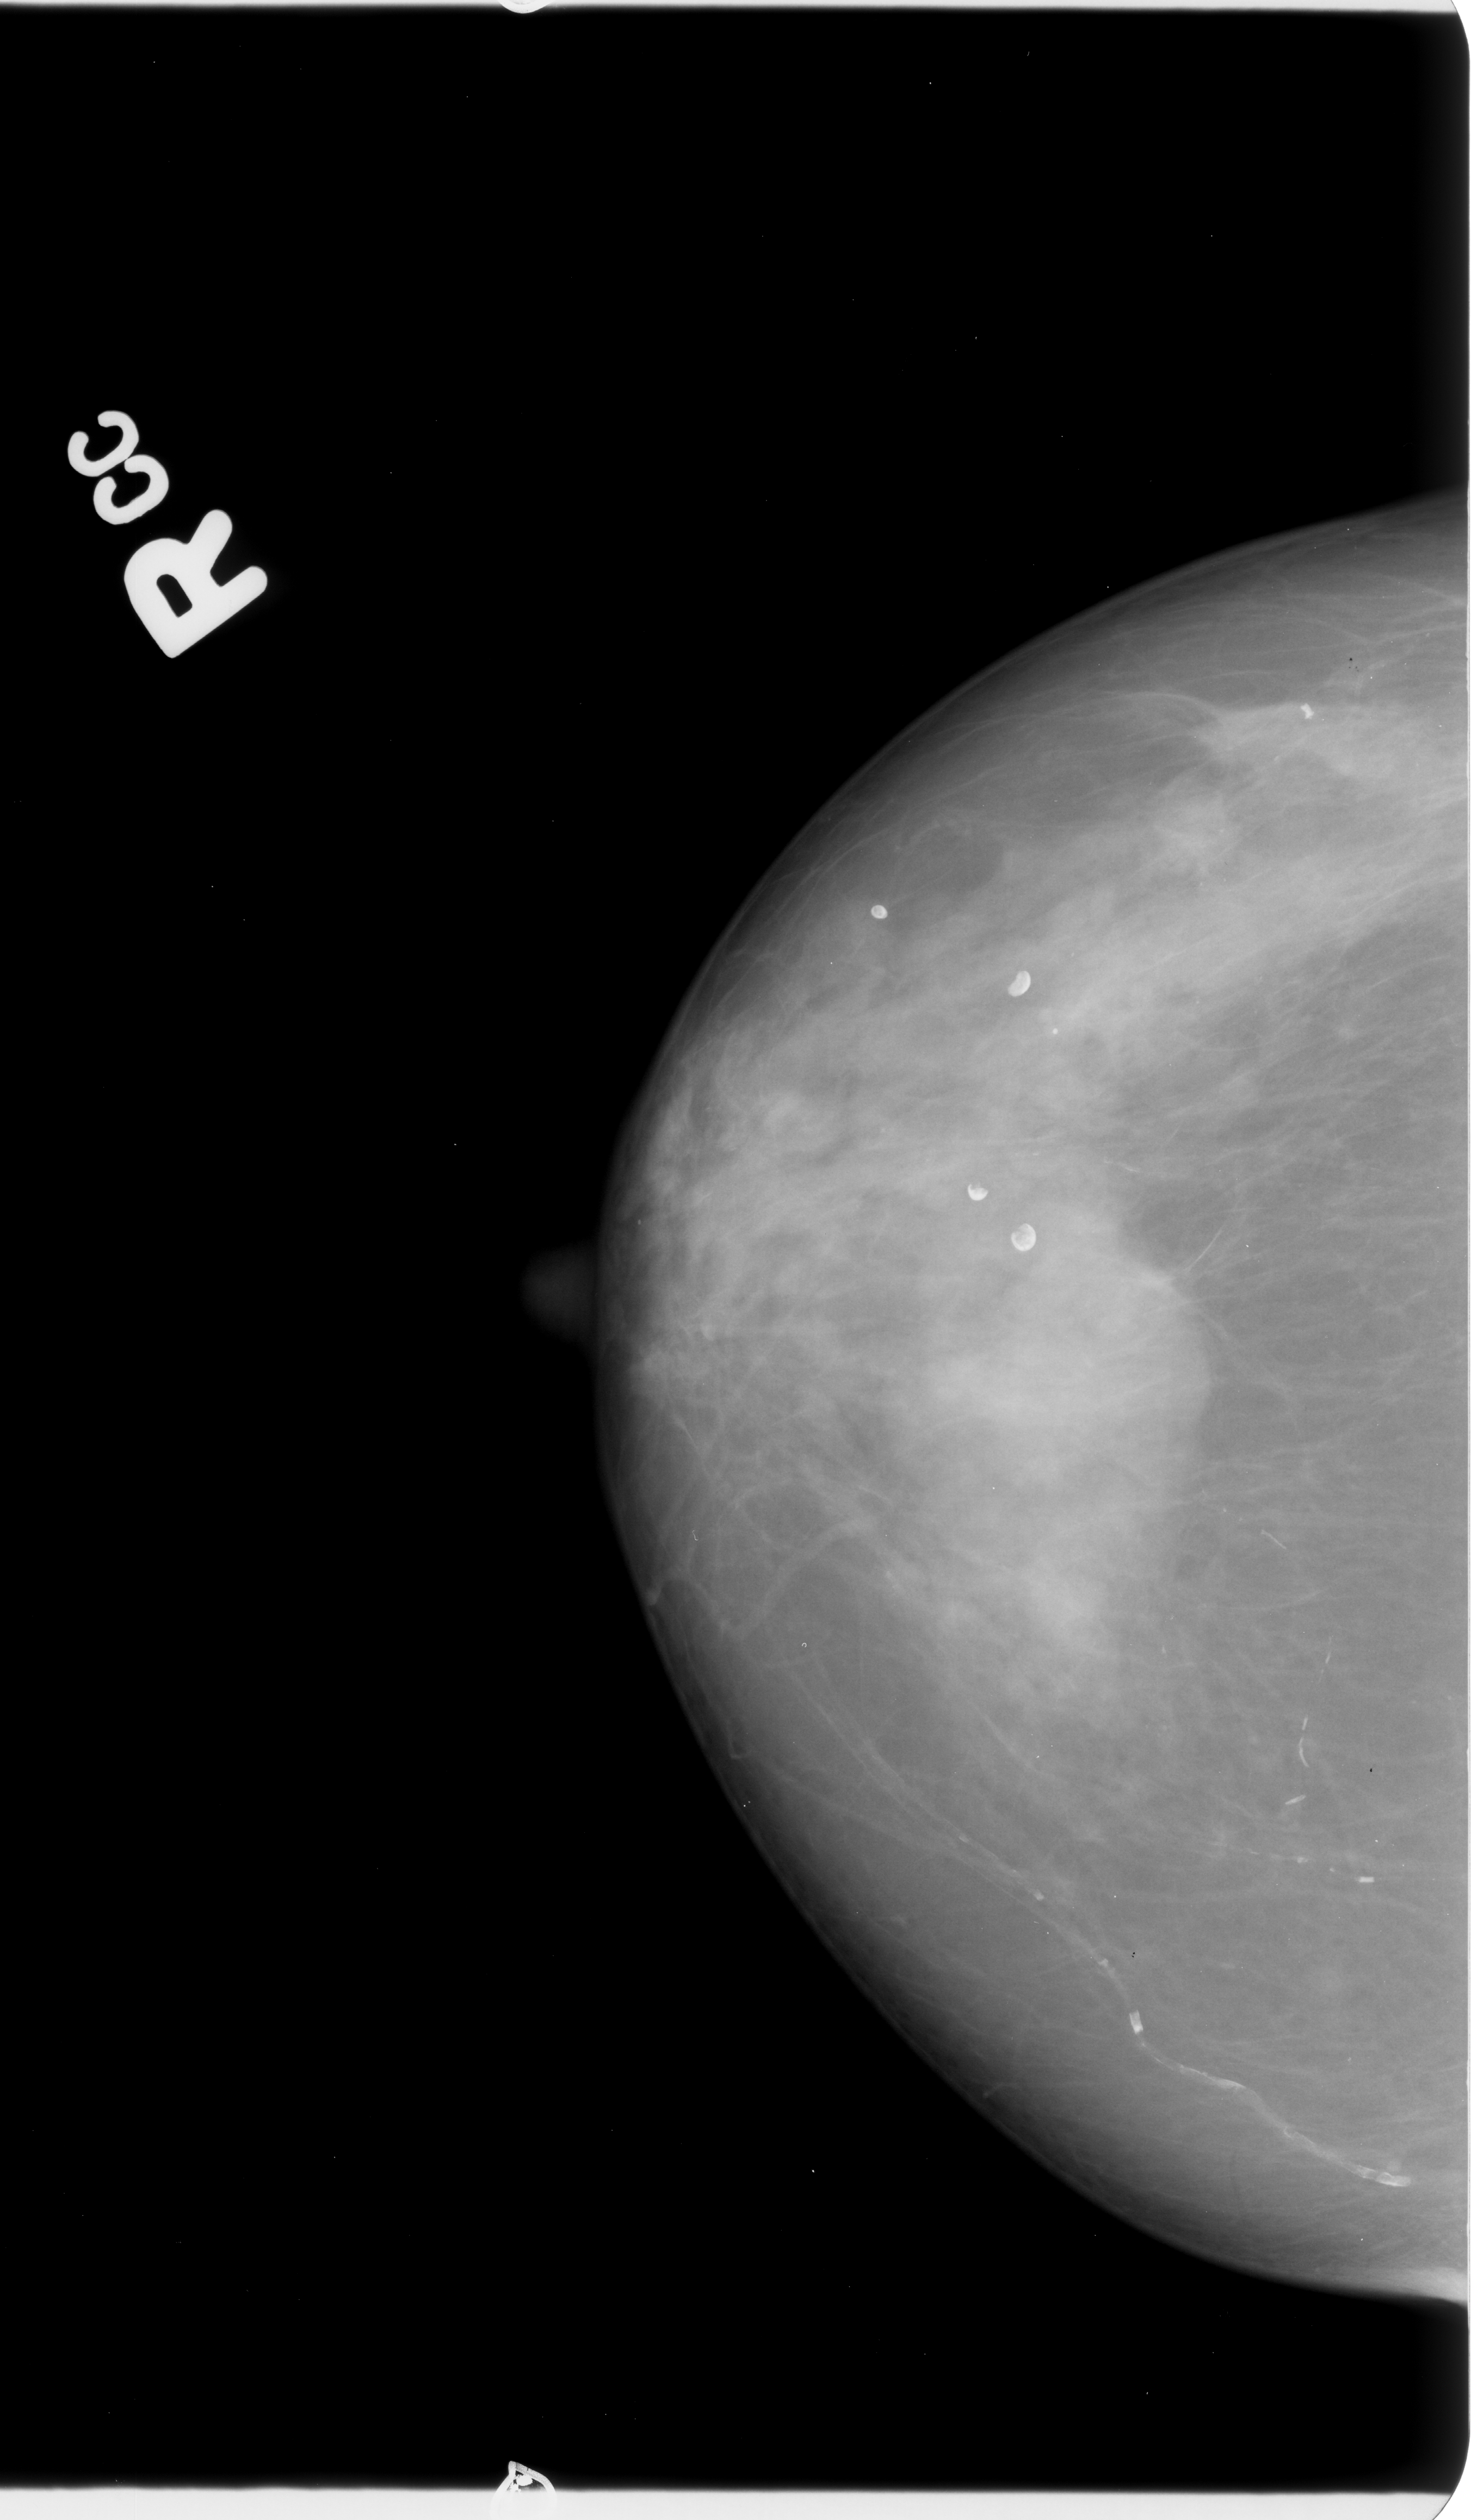
Mammogram (digitized film); right breast; CC view; BI-RADS breast density category 3 (scale 1–4); 1471 × 2520 image matrix.
Expert-marked regions of interest on this film, with their recorded descriptors:
- mass, shape oval, margins circumscribed / obscured; BI-RADS assessment category 3; pathology result (as recorded, not read from the image): malignant: bounding box (x1, y1, x2, y2) in pixels: (985, 1286, 1211, 1473)